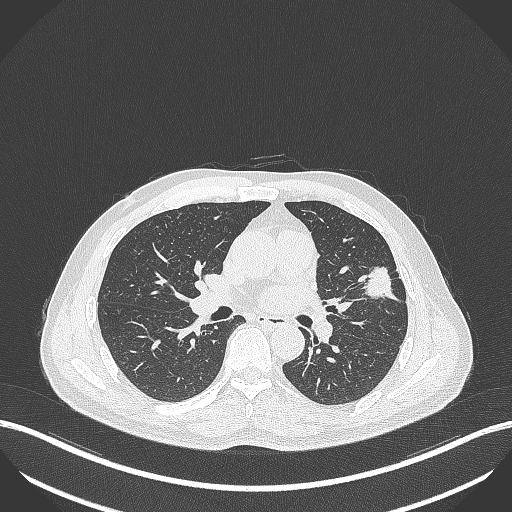
Chest CT, one axial slice; slice 217 of 418 in the series (ordered by position); reconstruction kernel B70f; lung window (W 1500 / L -600 HU); 1 mm slice thickness; 512 × 512 image matrix, field of view 400 × 400 mm. Patient: male, 55 years. From the clinical record (not read from this slice): clinical TNM (as recorded): T1c N0 M0.
Outlined on this slice (rectangle marked by the reading radiologist):
- lung tumour (recorded histology: adenocarcinoma): bounding box <356,262,401,303> (left, top, right, bottom; pixels)